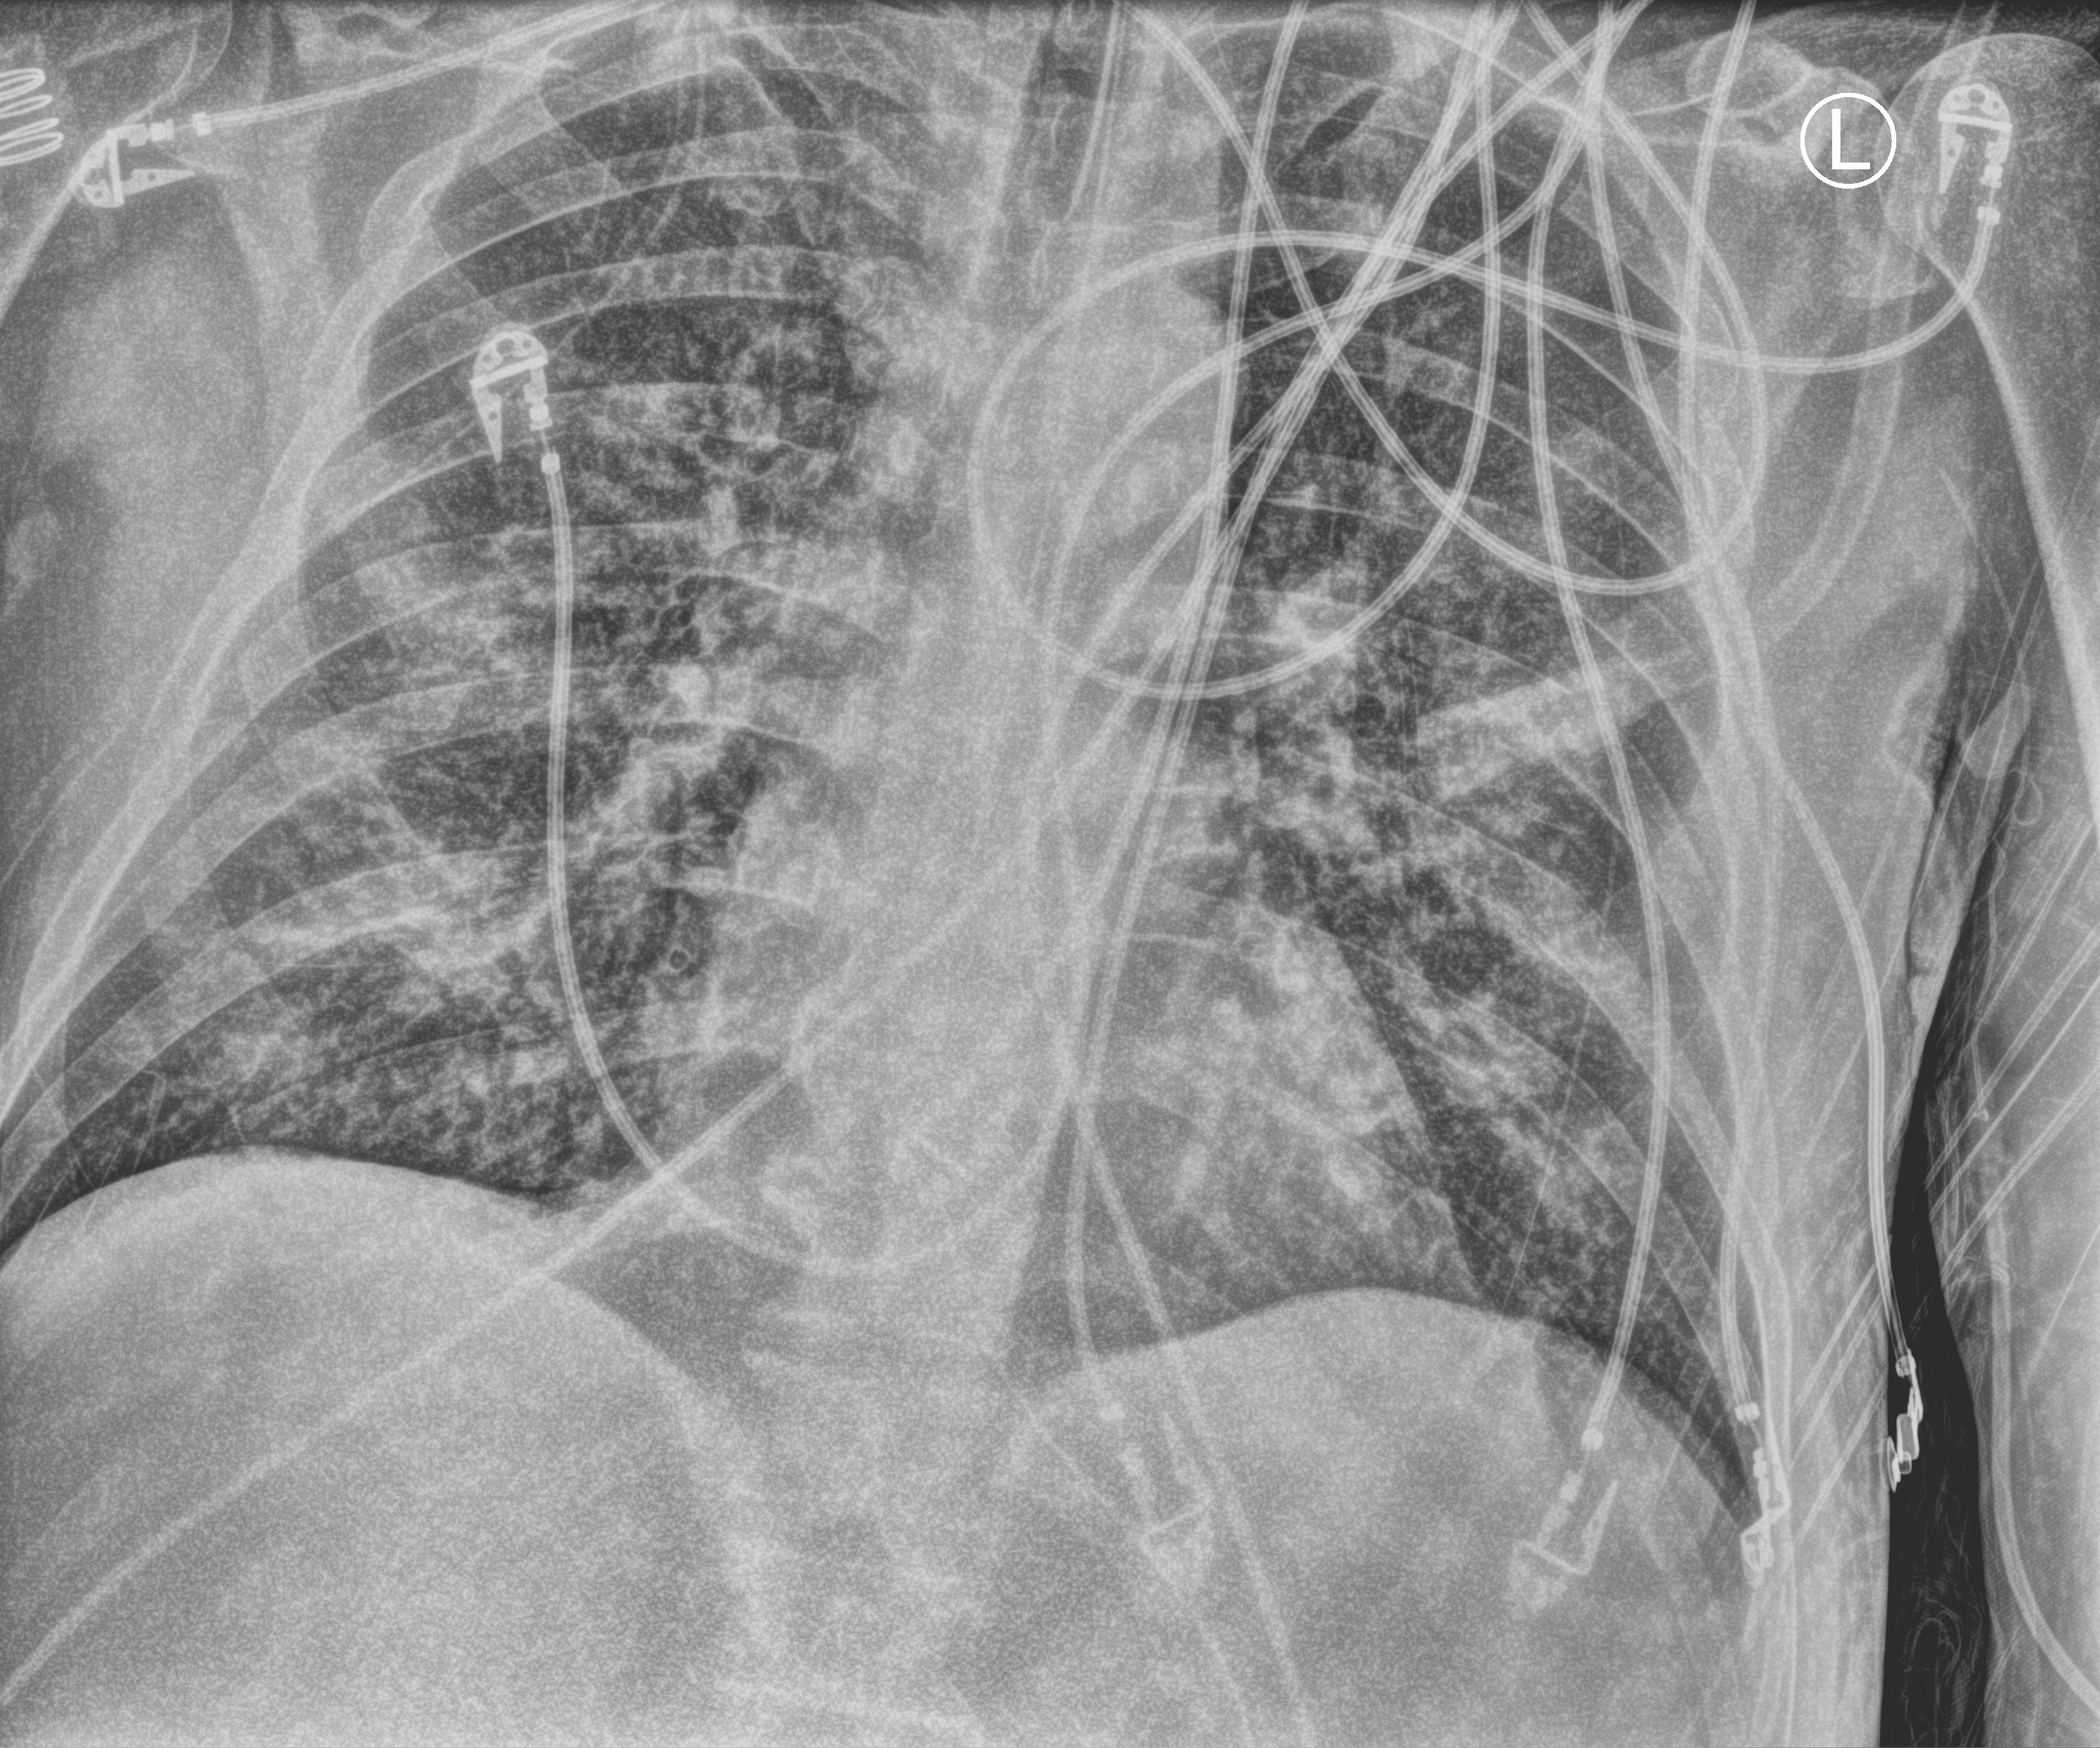
Portable chest radiograph; anteroposterior (AP) projection. Male patient hospitalised with COVID-19, age 18–59 years.
From the hospital-stay record, not from the radiograph (when in the stay this image was taken is not recorded): length of hospital stay: 19 days; mechanically ventilated during this hospital stay: yes; admitted to intensive care during this hospital stay: no.